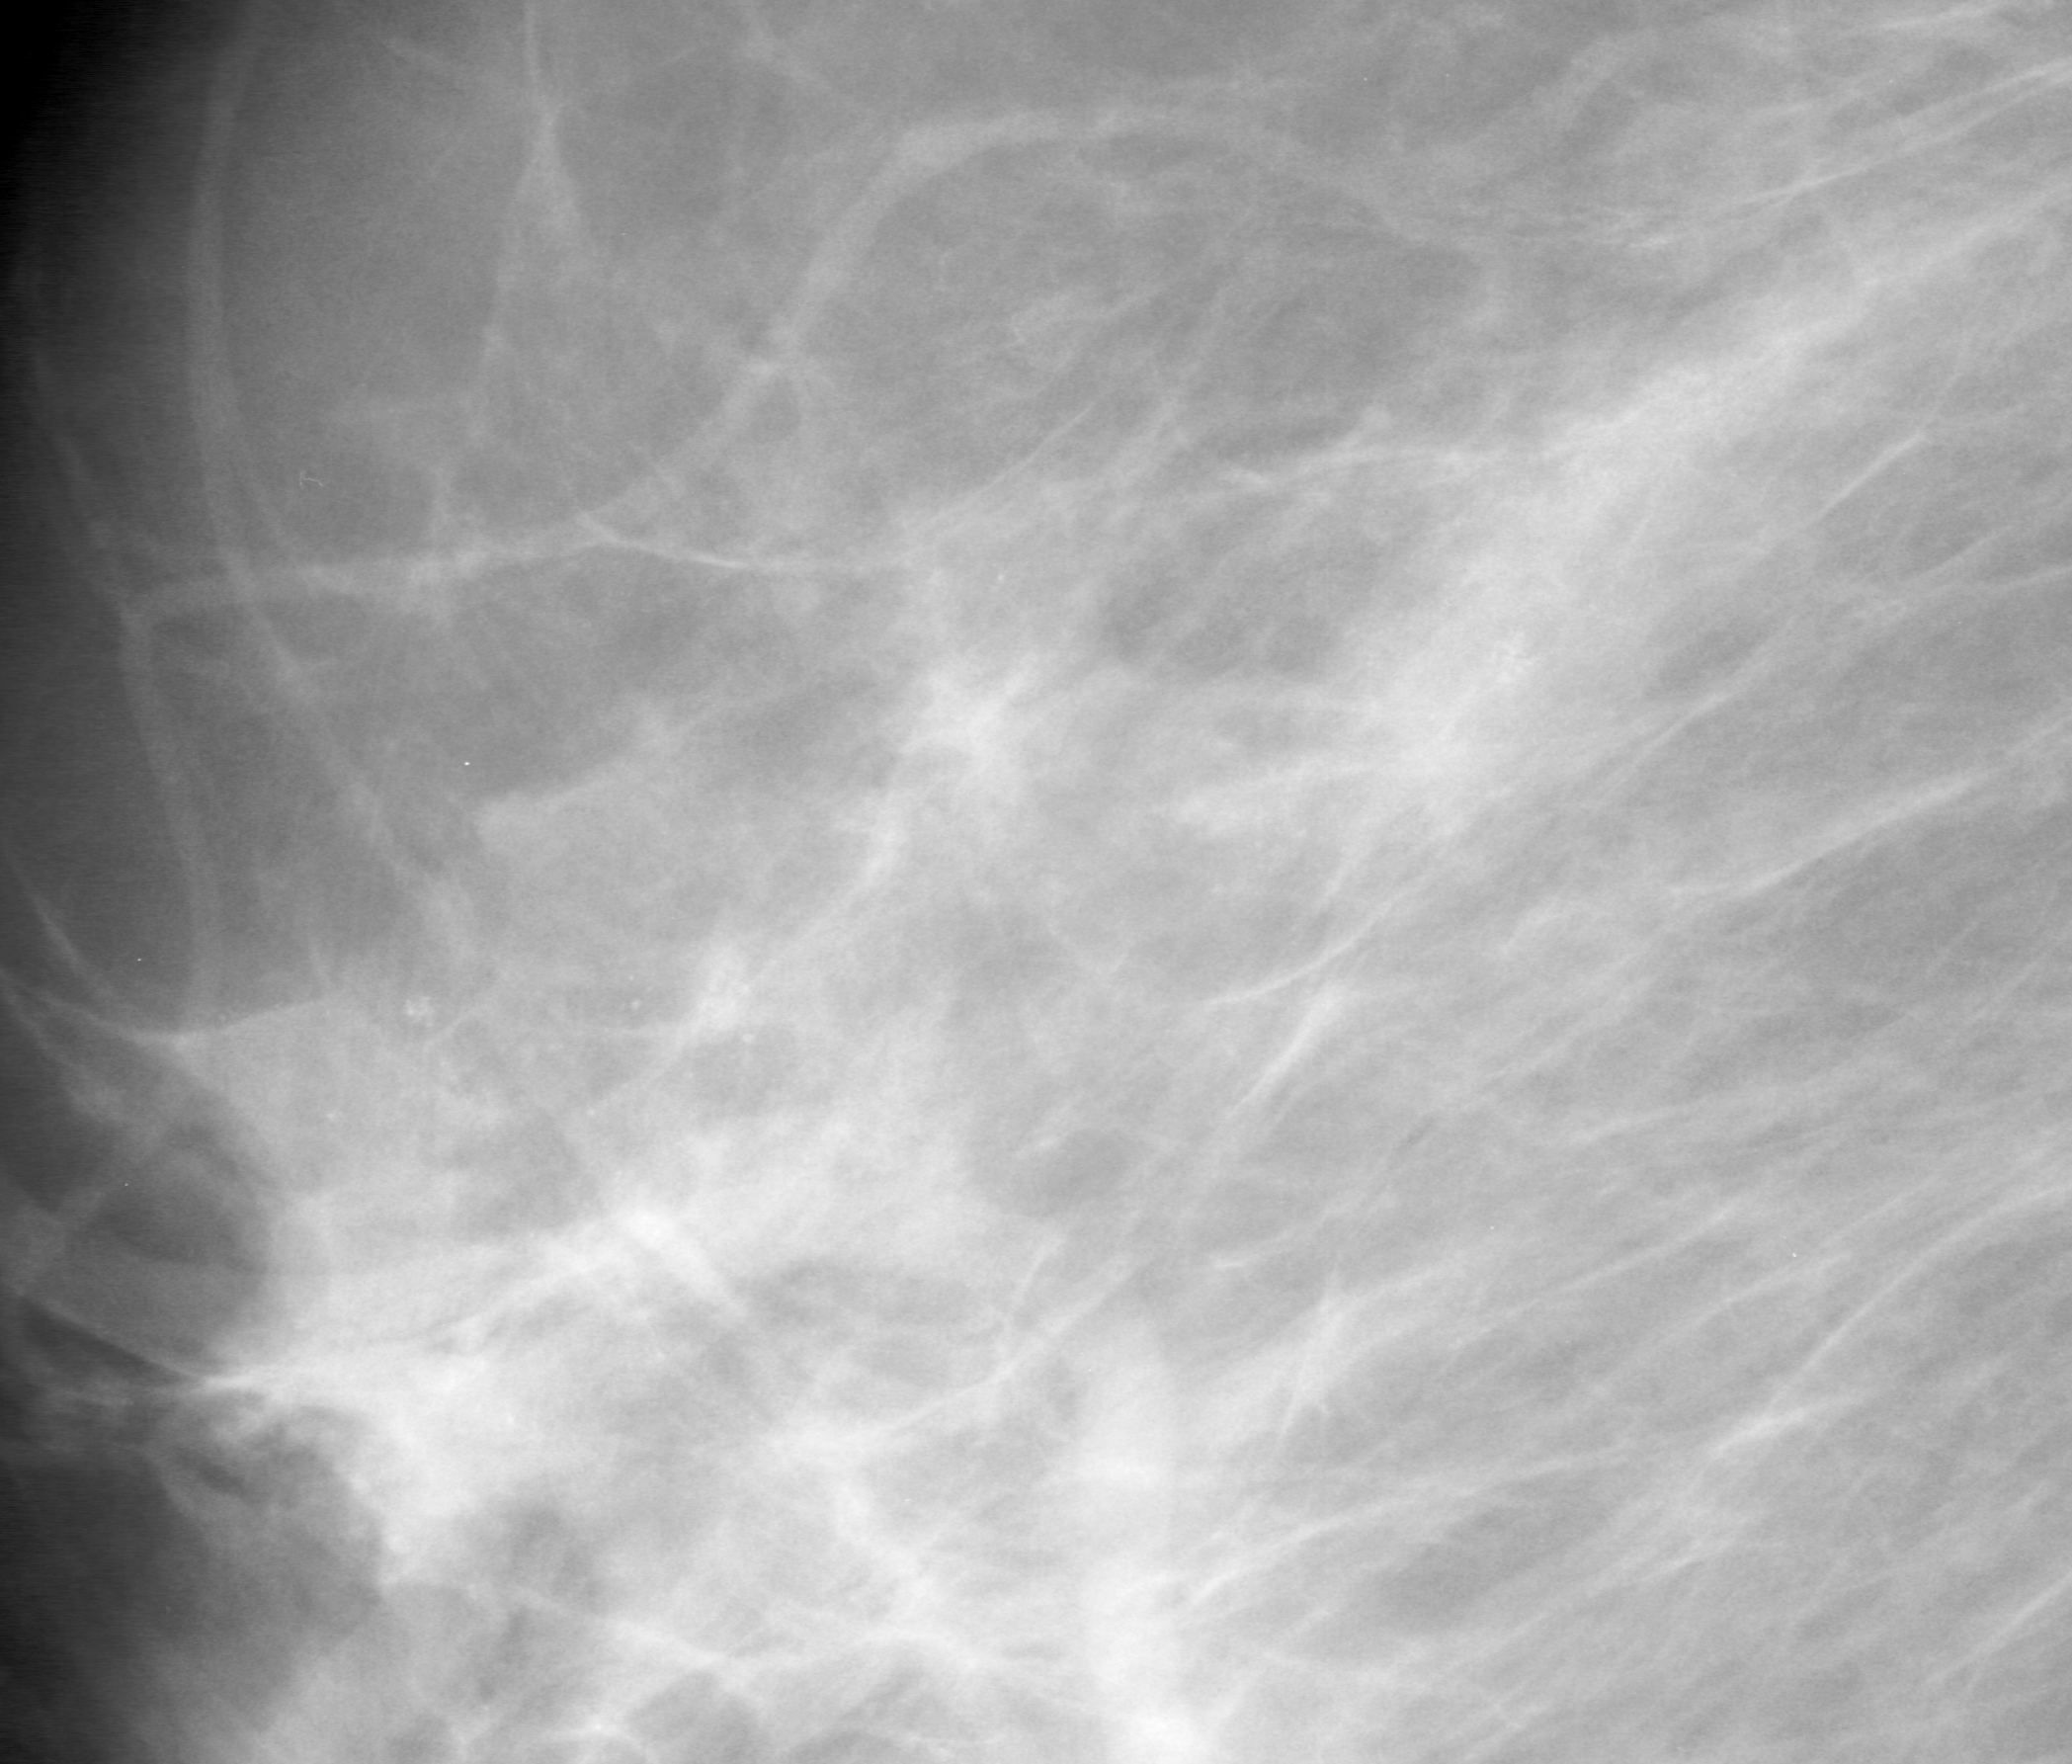
Cropped region of a digitized screen-film mammogram centred on a radiologist-marked abnormality, right breast, MLO view, BI-RADS breast density category 2 (scale 1–4).
Calcifications, morphology amorphous, distribution segmental; BI-RADS assessment category 0 (incomplete: needs additional imaging); pathology (as recorded): malignant.